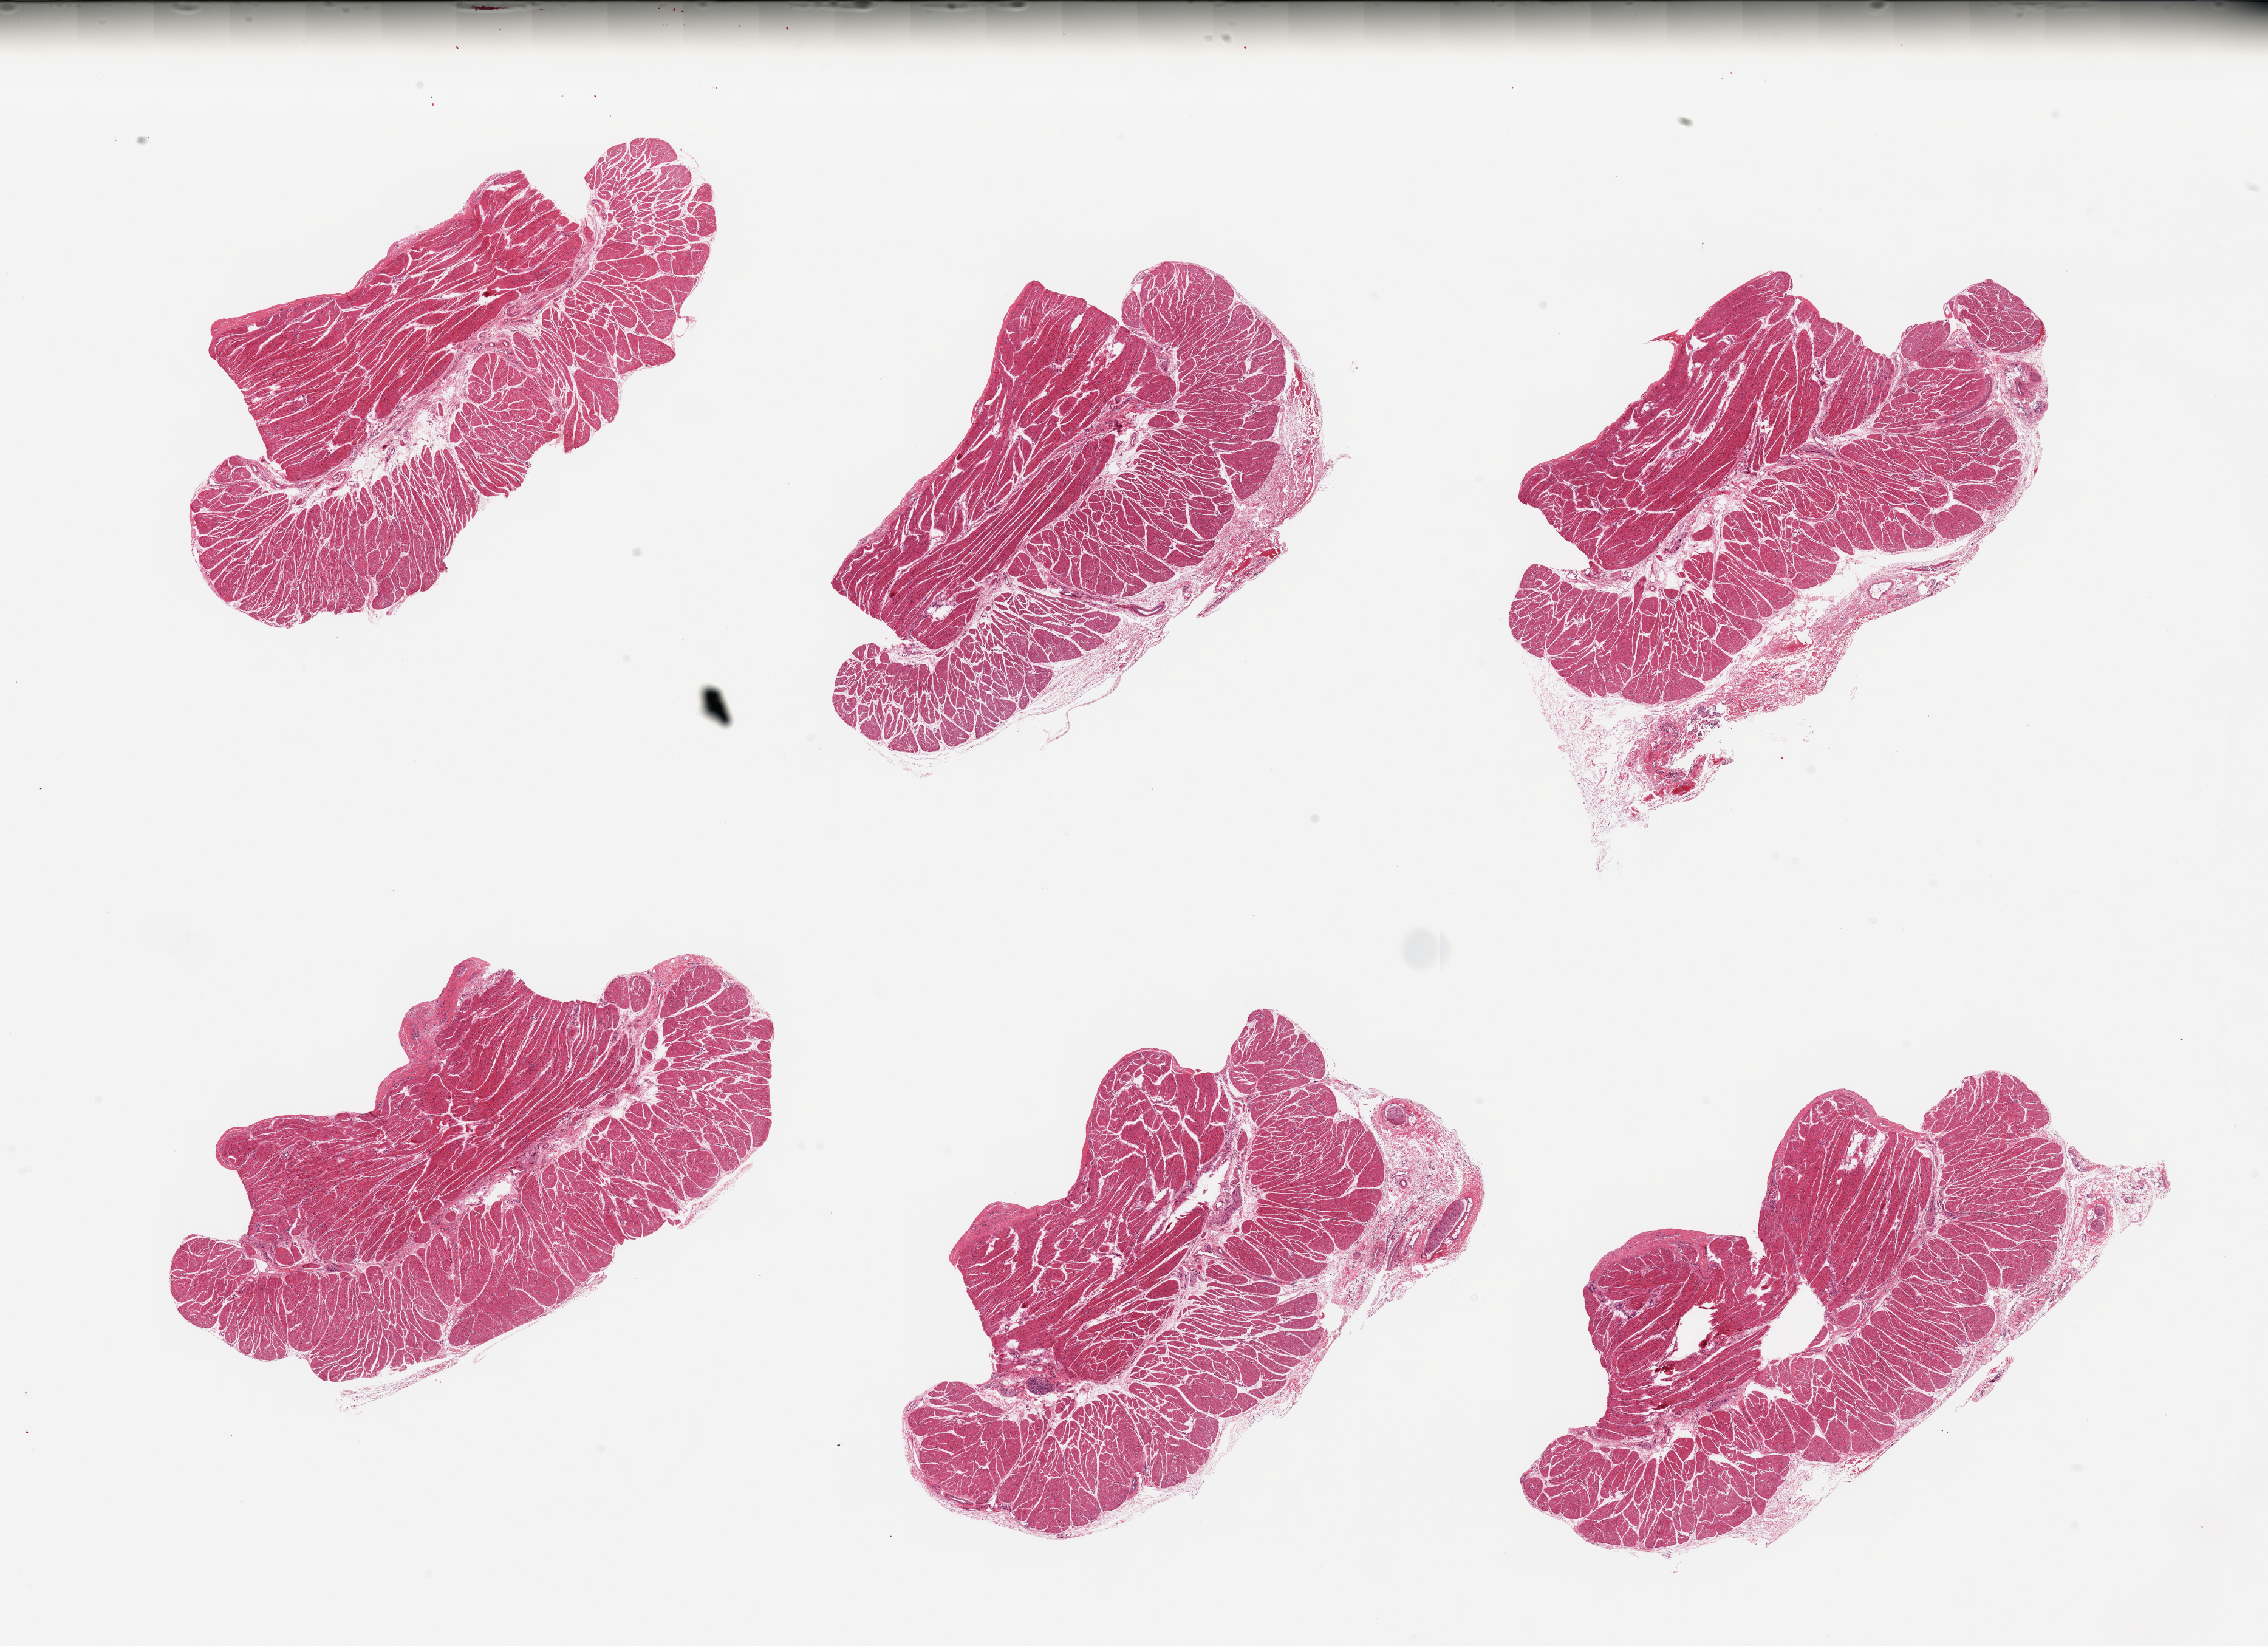
Digitized hematoxylin and eosin (H&E)-stained section, low-resolution overview of the scanned area, about 29.5 x 21.4 mm (acquisition: 20x scan), PAXgene-fixed, paraffin-embedded tissue, target tissue: esophageal muscle, tissue donor sample. Donor: female.
• review note (as recorded): 6 pieces; well dissected